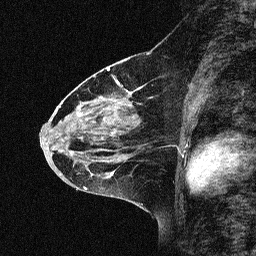
Breast MRI (dynamic contrast-enhanced), one sagittal slice; slice 32 of 64 in the series (ordered by position); dynamic contrast-enhanced study with each time point stored as its own series, time point 2 of 3 at this slice position (early post-contrast, ordered by acquisition time); 1.5 T; TE 4.5 ms, TR 11 ms; 256 × 256 image matrix, field of view 200 × 200 mm. Patient: female, 46 years. Case-level facts recorded for this patient, not image findings: setting: breast cancer imaged before/during neoadjuvant chemotherapy; receptor status: HER2-positive.
Outlined on this slice (semi-automatic segmentation, software-assisted and operator-edited):
- analysis volume of interest (the breast-tissue region the enhancement analysis was run in; not a lesion): bounding box <46,51,180,169> (left, top, right, bottom; pixels)
- tumour enhancement mask (voxels above the 90 % enhancement threshold inside the analysis volume of interest): <119,85,140,107>